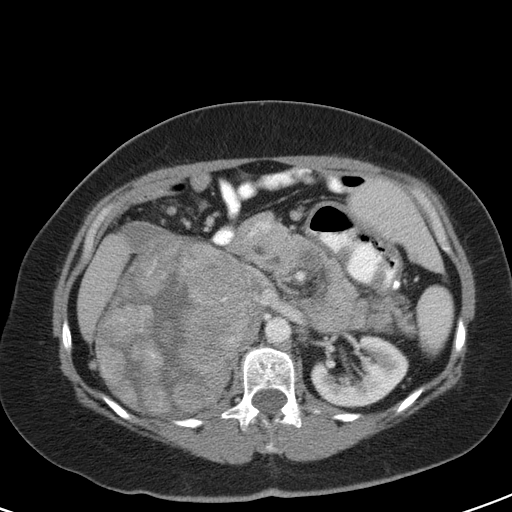
Contrast-enhanced abdominal CT, one axial slice; soft-tissue window (W 400 / L 40 HU); 512 × 512 image matrix, field of view 356 × 356 mm. Female patient, age 51 years. Case-level facts recorded for this patient, not image findings: diagnosis: adrenocortical carcinoma; tumour side: right adrenal; tumour size at pathology: 17 cm; Ki-67 index: 12 %; stage (as recorded): 2.
Outlined on this slice (semi-automatically segmented with operator editing):
- mass: box from (x=97, y=221) to (x=254, y=416) px